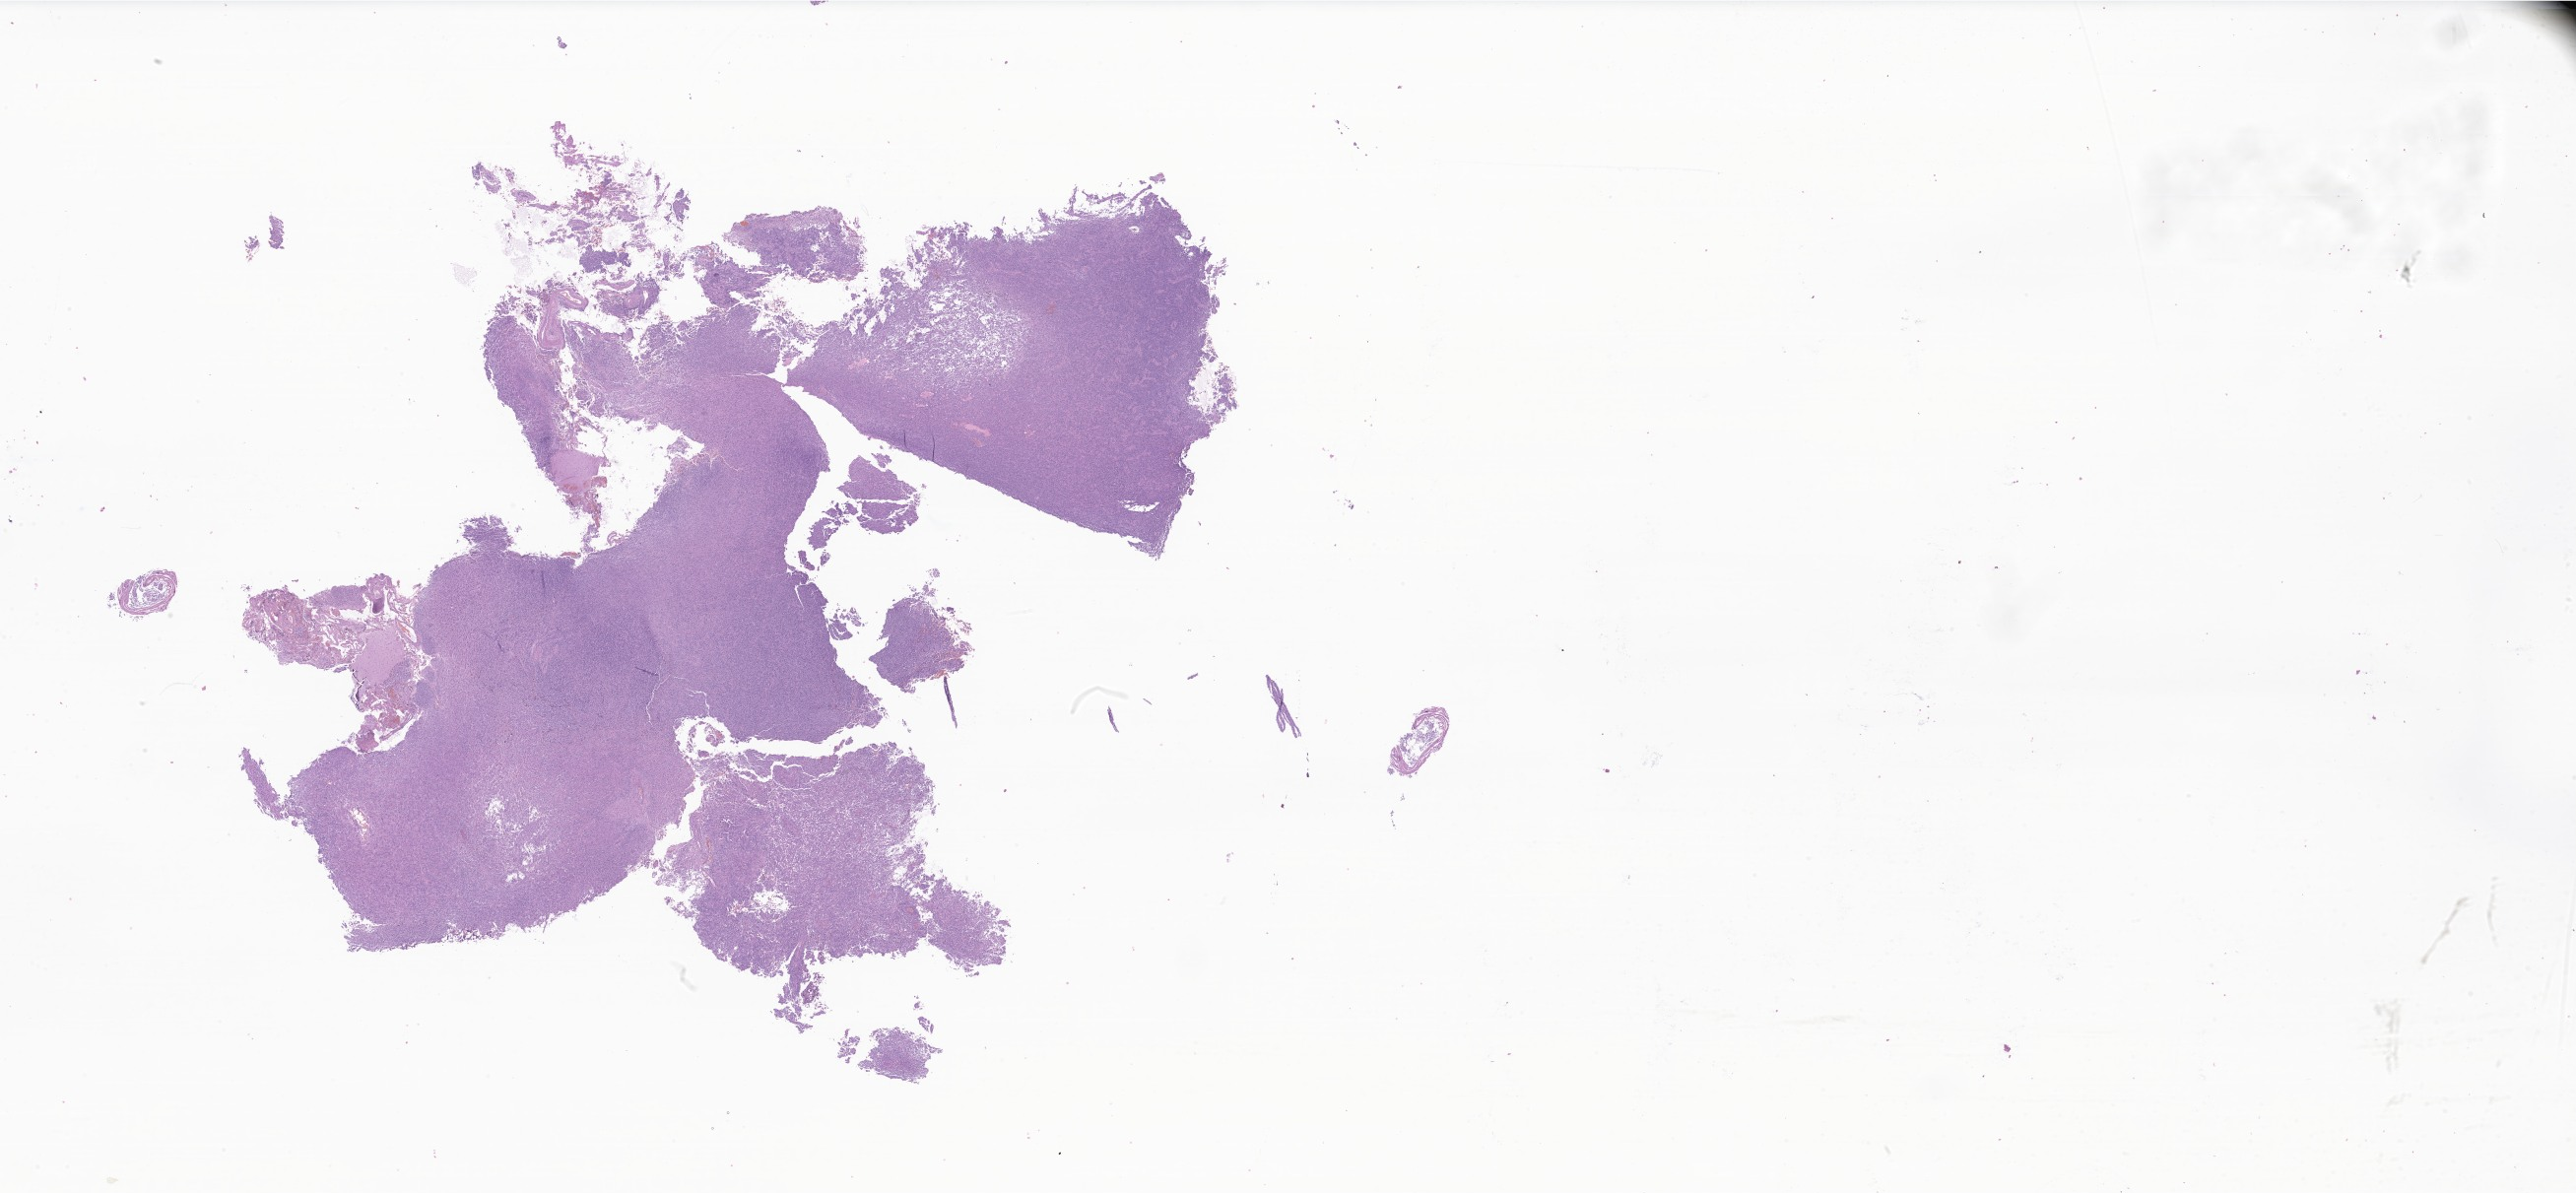
Whole-slide image, hematoxylin and eosin (H&E) stain of tumor tissue from the temporal lobe — shown as a low-resolution overview of the whole scanned area (about 44.1 x 20.4 mm); FFPE section. Female patient, age 97 months (8 years 1 month).
Diagnosis (ICD-O-3 morphology term): Glioma, malignant.